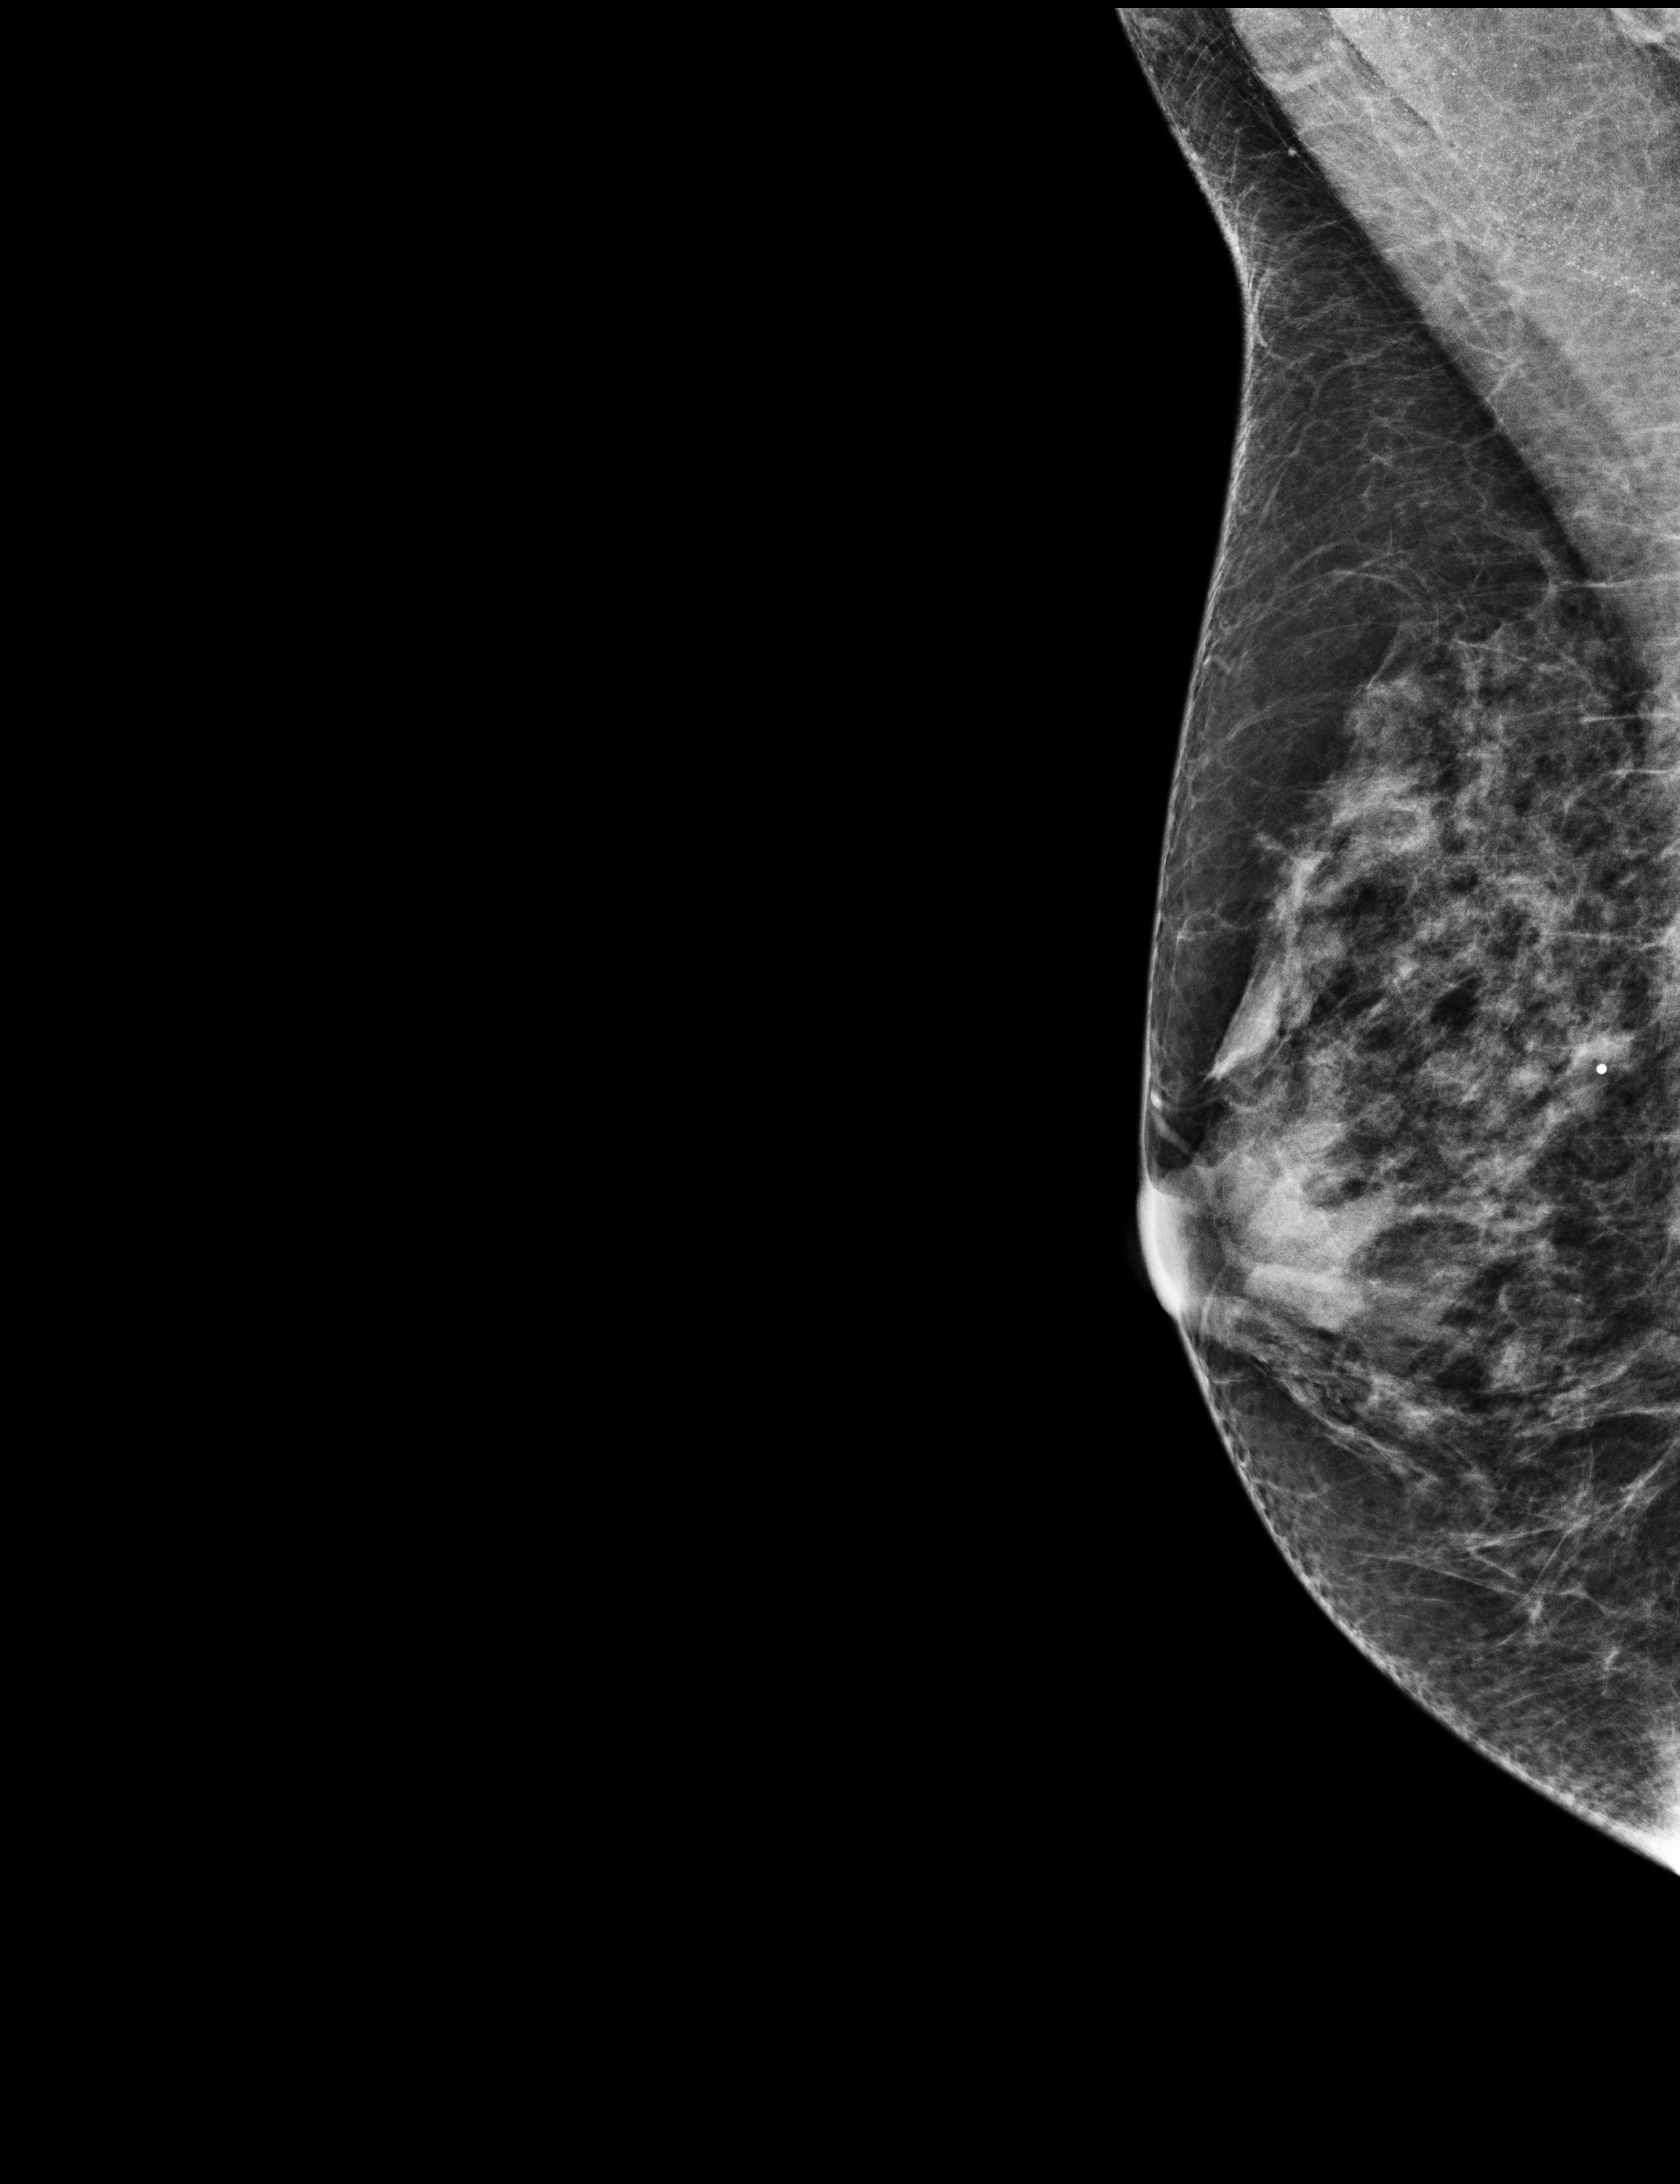
Digital mammogram (FFDM); right breast; medio-lateral oblique projection; annual screening mammography examination; compressed breast thickness 41 mm; system: Selenia Dimensions. Female patient, age 59 years.
Final BI-RADS category for the screening round (tomosynthesis exam, both breasts): category 1.